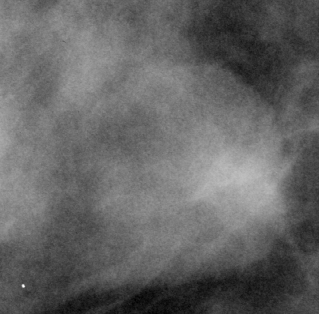
Crop from a digitized film mammogram around one marked abnormality; right breast; MLO view; BI-RADS breast density category 2 (scale 1–4).
Finding: mass, shape round, margins obscured; BI-RADS assessment category 3; subtlety rating 4 on a 1 (subtle) to 5 (obvious) scale; pathology (as recorded): benign.